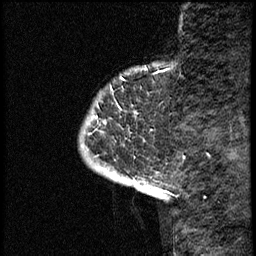
Breast MRI (dynamic contrast-enhanced), one sagittal slice; position 5 of 68 along the scan axis; dynamic contrast-enhanced study with each time point stored as its own series, time point 2 of 3 at this slice position (early post-contrast, ordered by acquisition time); 1.5 T; TE 4.2 ms, TR 17.6 ms; 2 mm slice thickness; 256 × 256 image matrix, field of view 200 × 200 mm. Female patient, age 52 years. Case-level facts recorded for this patient, not image findings: setting: breast cancer imaged before/during neoadjuvant chemotherapy; receptor status: HER2-positive.
Structures marked on this image (semi-automatically segmented with operator editing):
- analysis volume of interest (the breast-tissue region the enhancement analysis was run in; not a lesion): bounding box (x1, y1, x2, y2) in pixels: (80, 61, 176, 184)
- tumour enhancement mask (voxels above the 100 % enhancement threshold inside the analysis volume of interest): (115, 72, 156, 184)